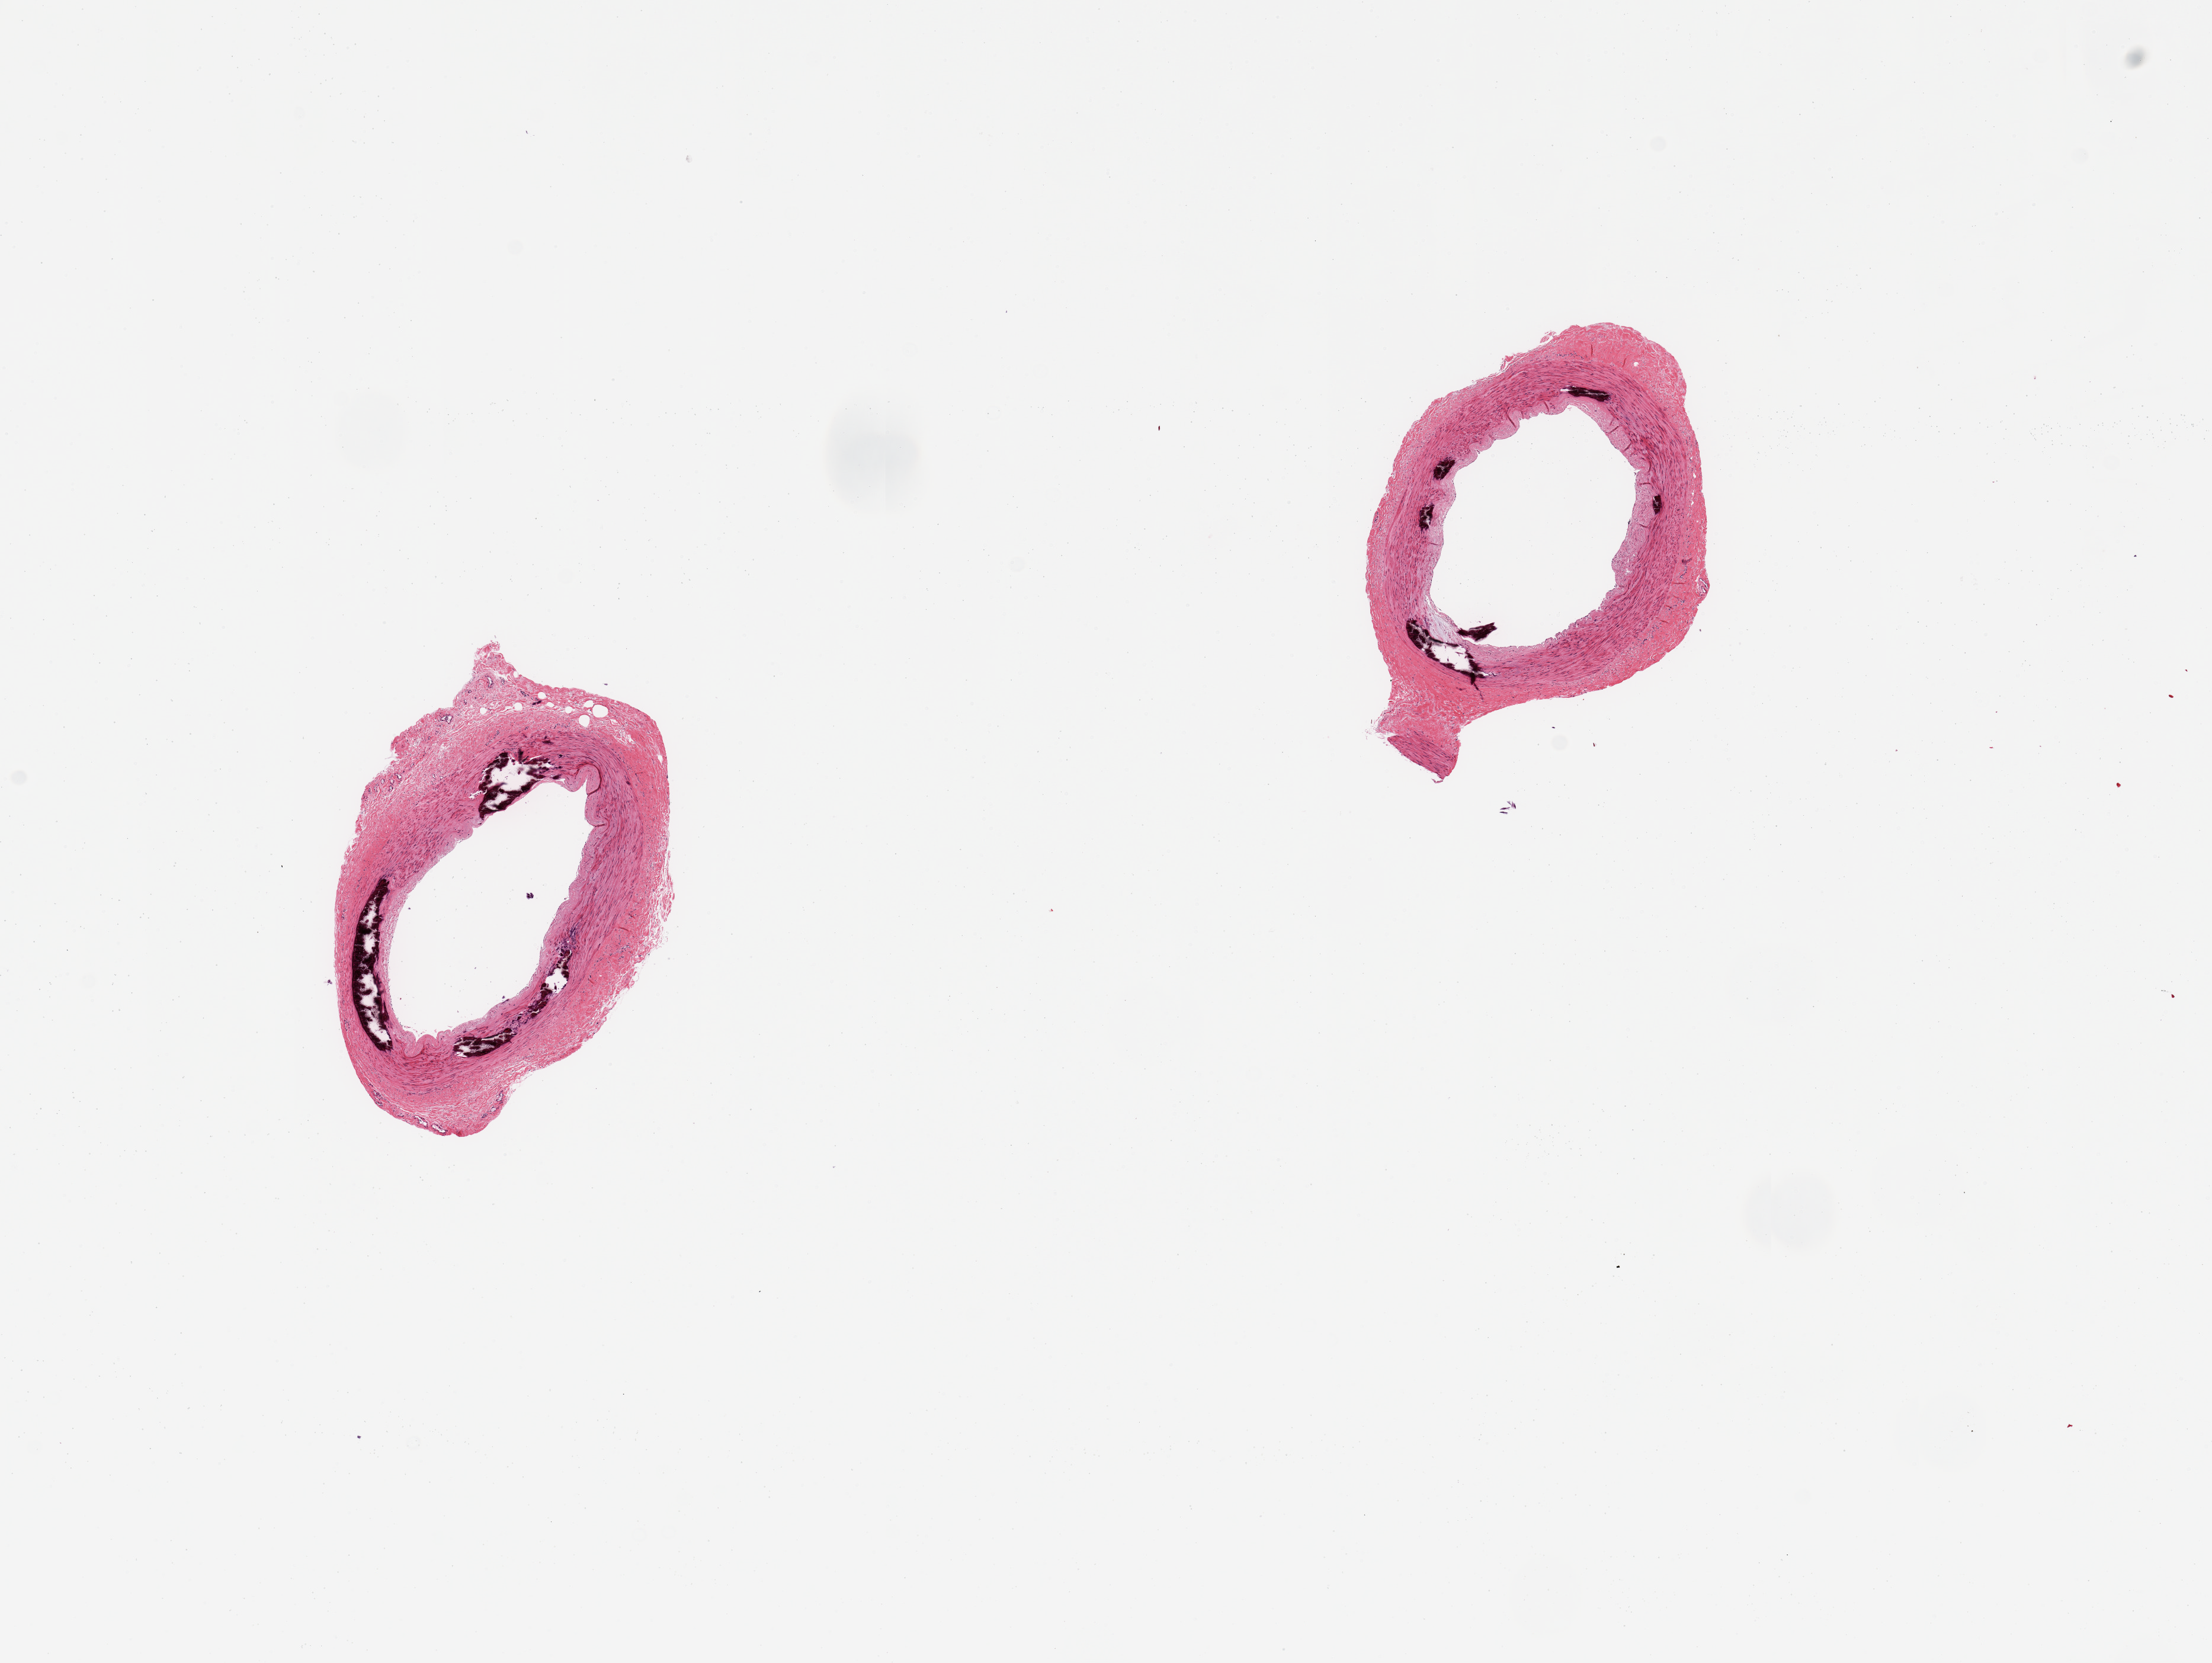
Whole-slide image, H&E stain, whole scanned area (about 14.8 x 11.1 mm, acquisition: 20x scan) shown as a low-resolution overview. PAXgene-fixed, paraffin-embedded tissue. Target tissue: tibial artery. Donor tissue sample. Donor: female.
Reviewer comment on this tissue sample: 2 pieces; extensive medial calcification.